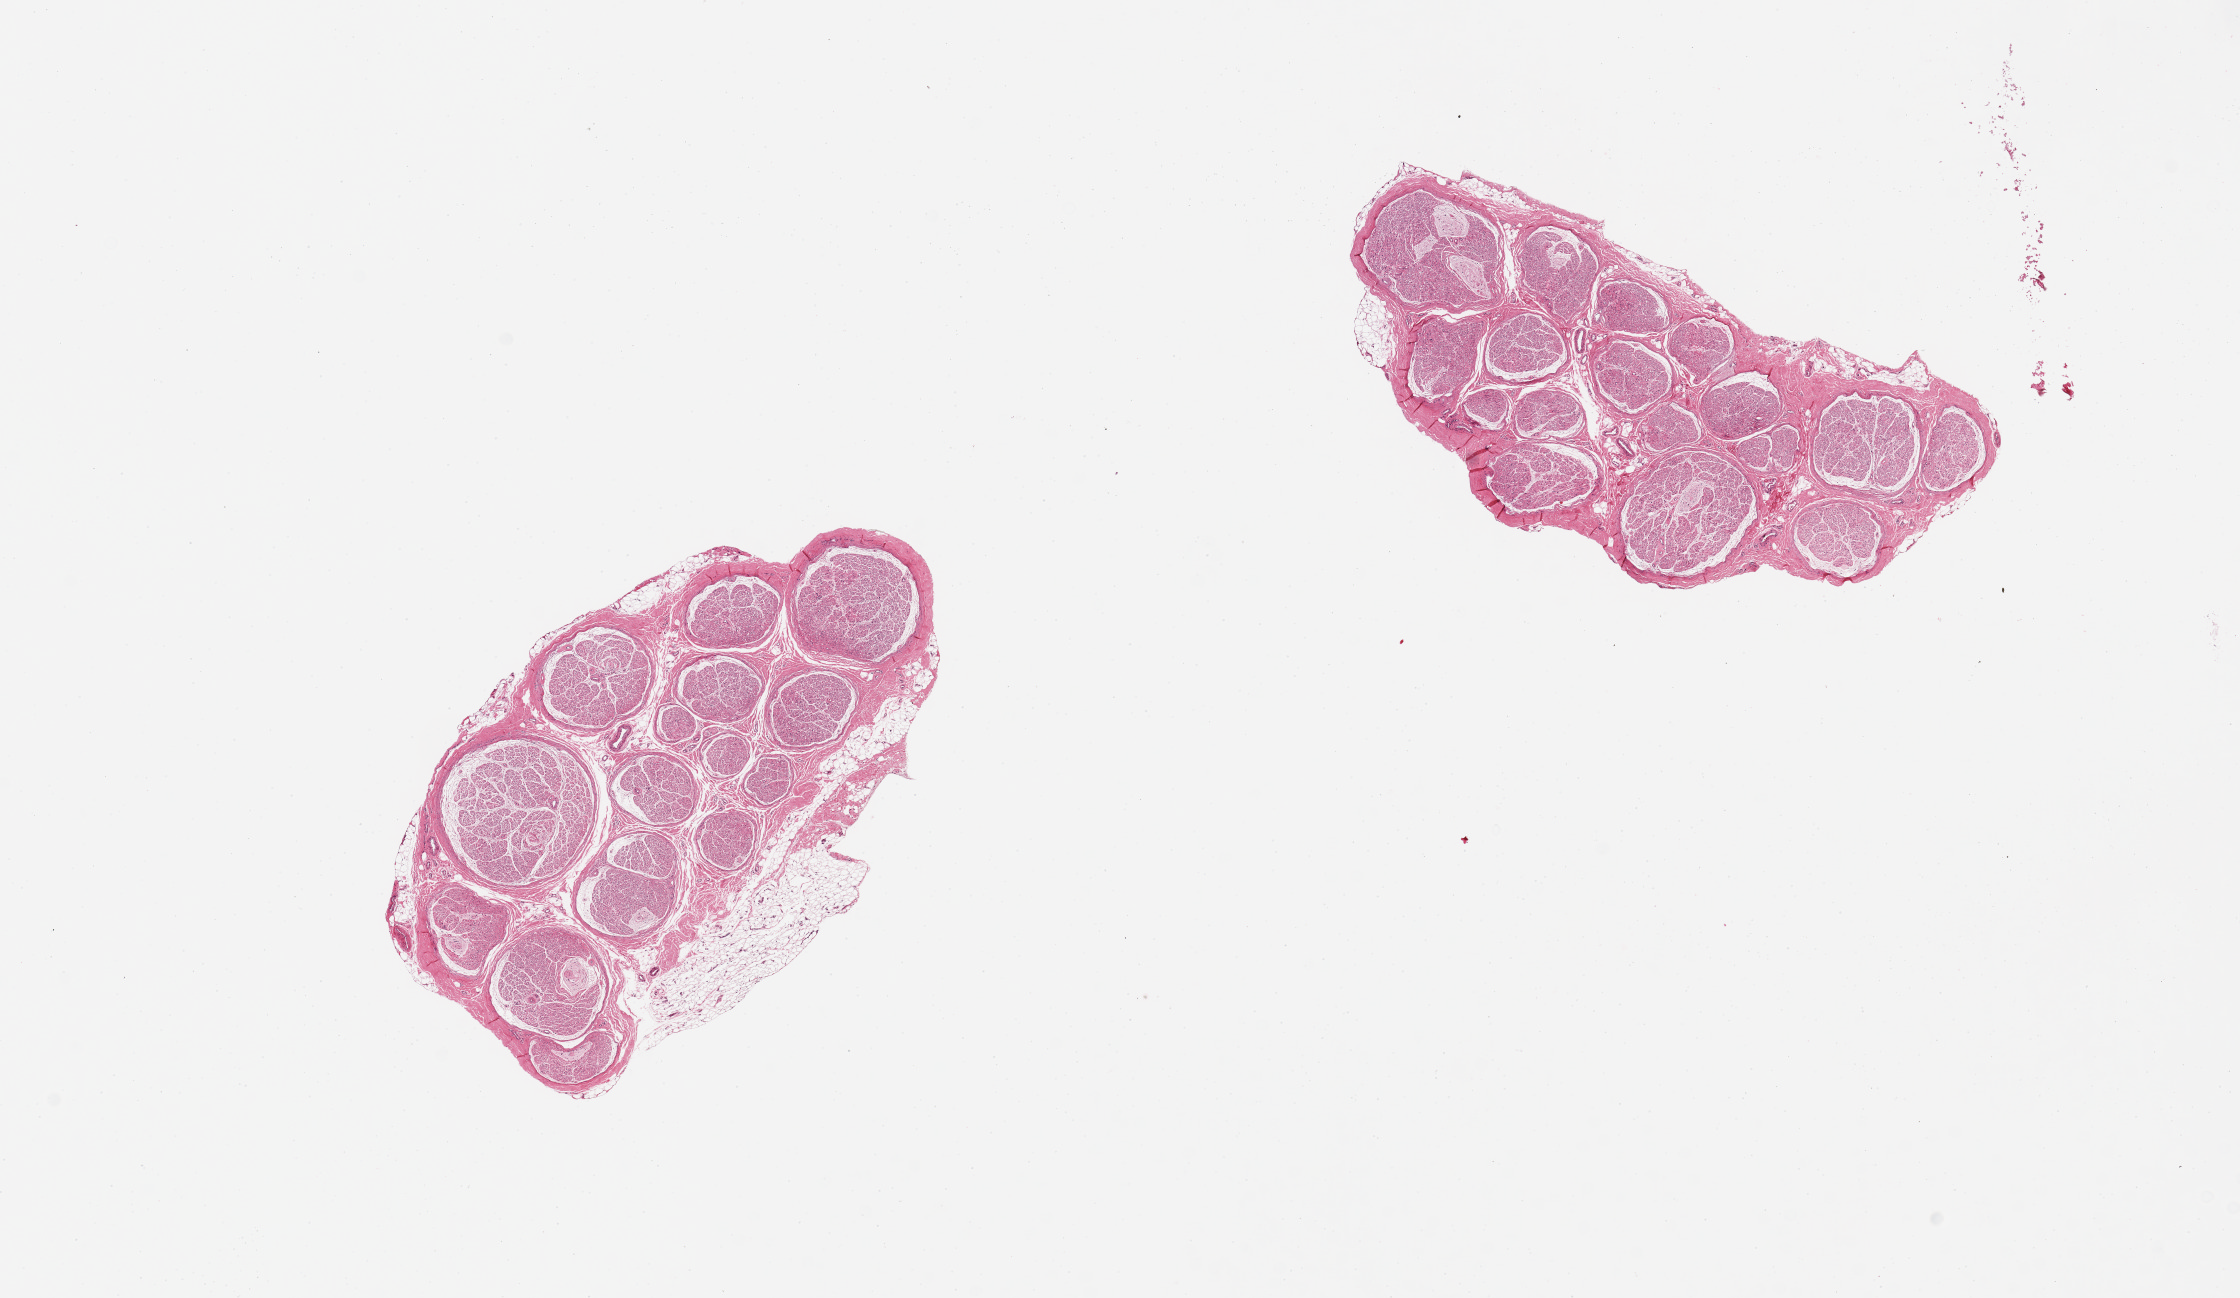
Digitized haematoxylin and eosin-stained section, shown as a low-resolution overview of the whole scanned area (about 17.7 x 10.3 mm). PAXgene-fixed, paraffin-embedded tissue. Section of tibial nerve (target tissue). Tissue donor sample. Male donor.
Pathologist's review note for this sample: 2 pieces, 5x3 & 5x3mm; 1 has 20% external adipose.